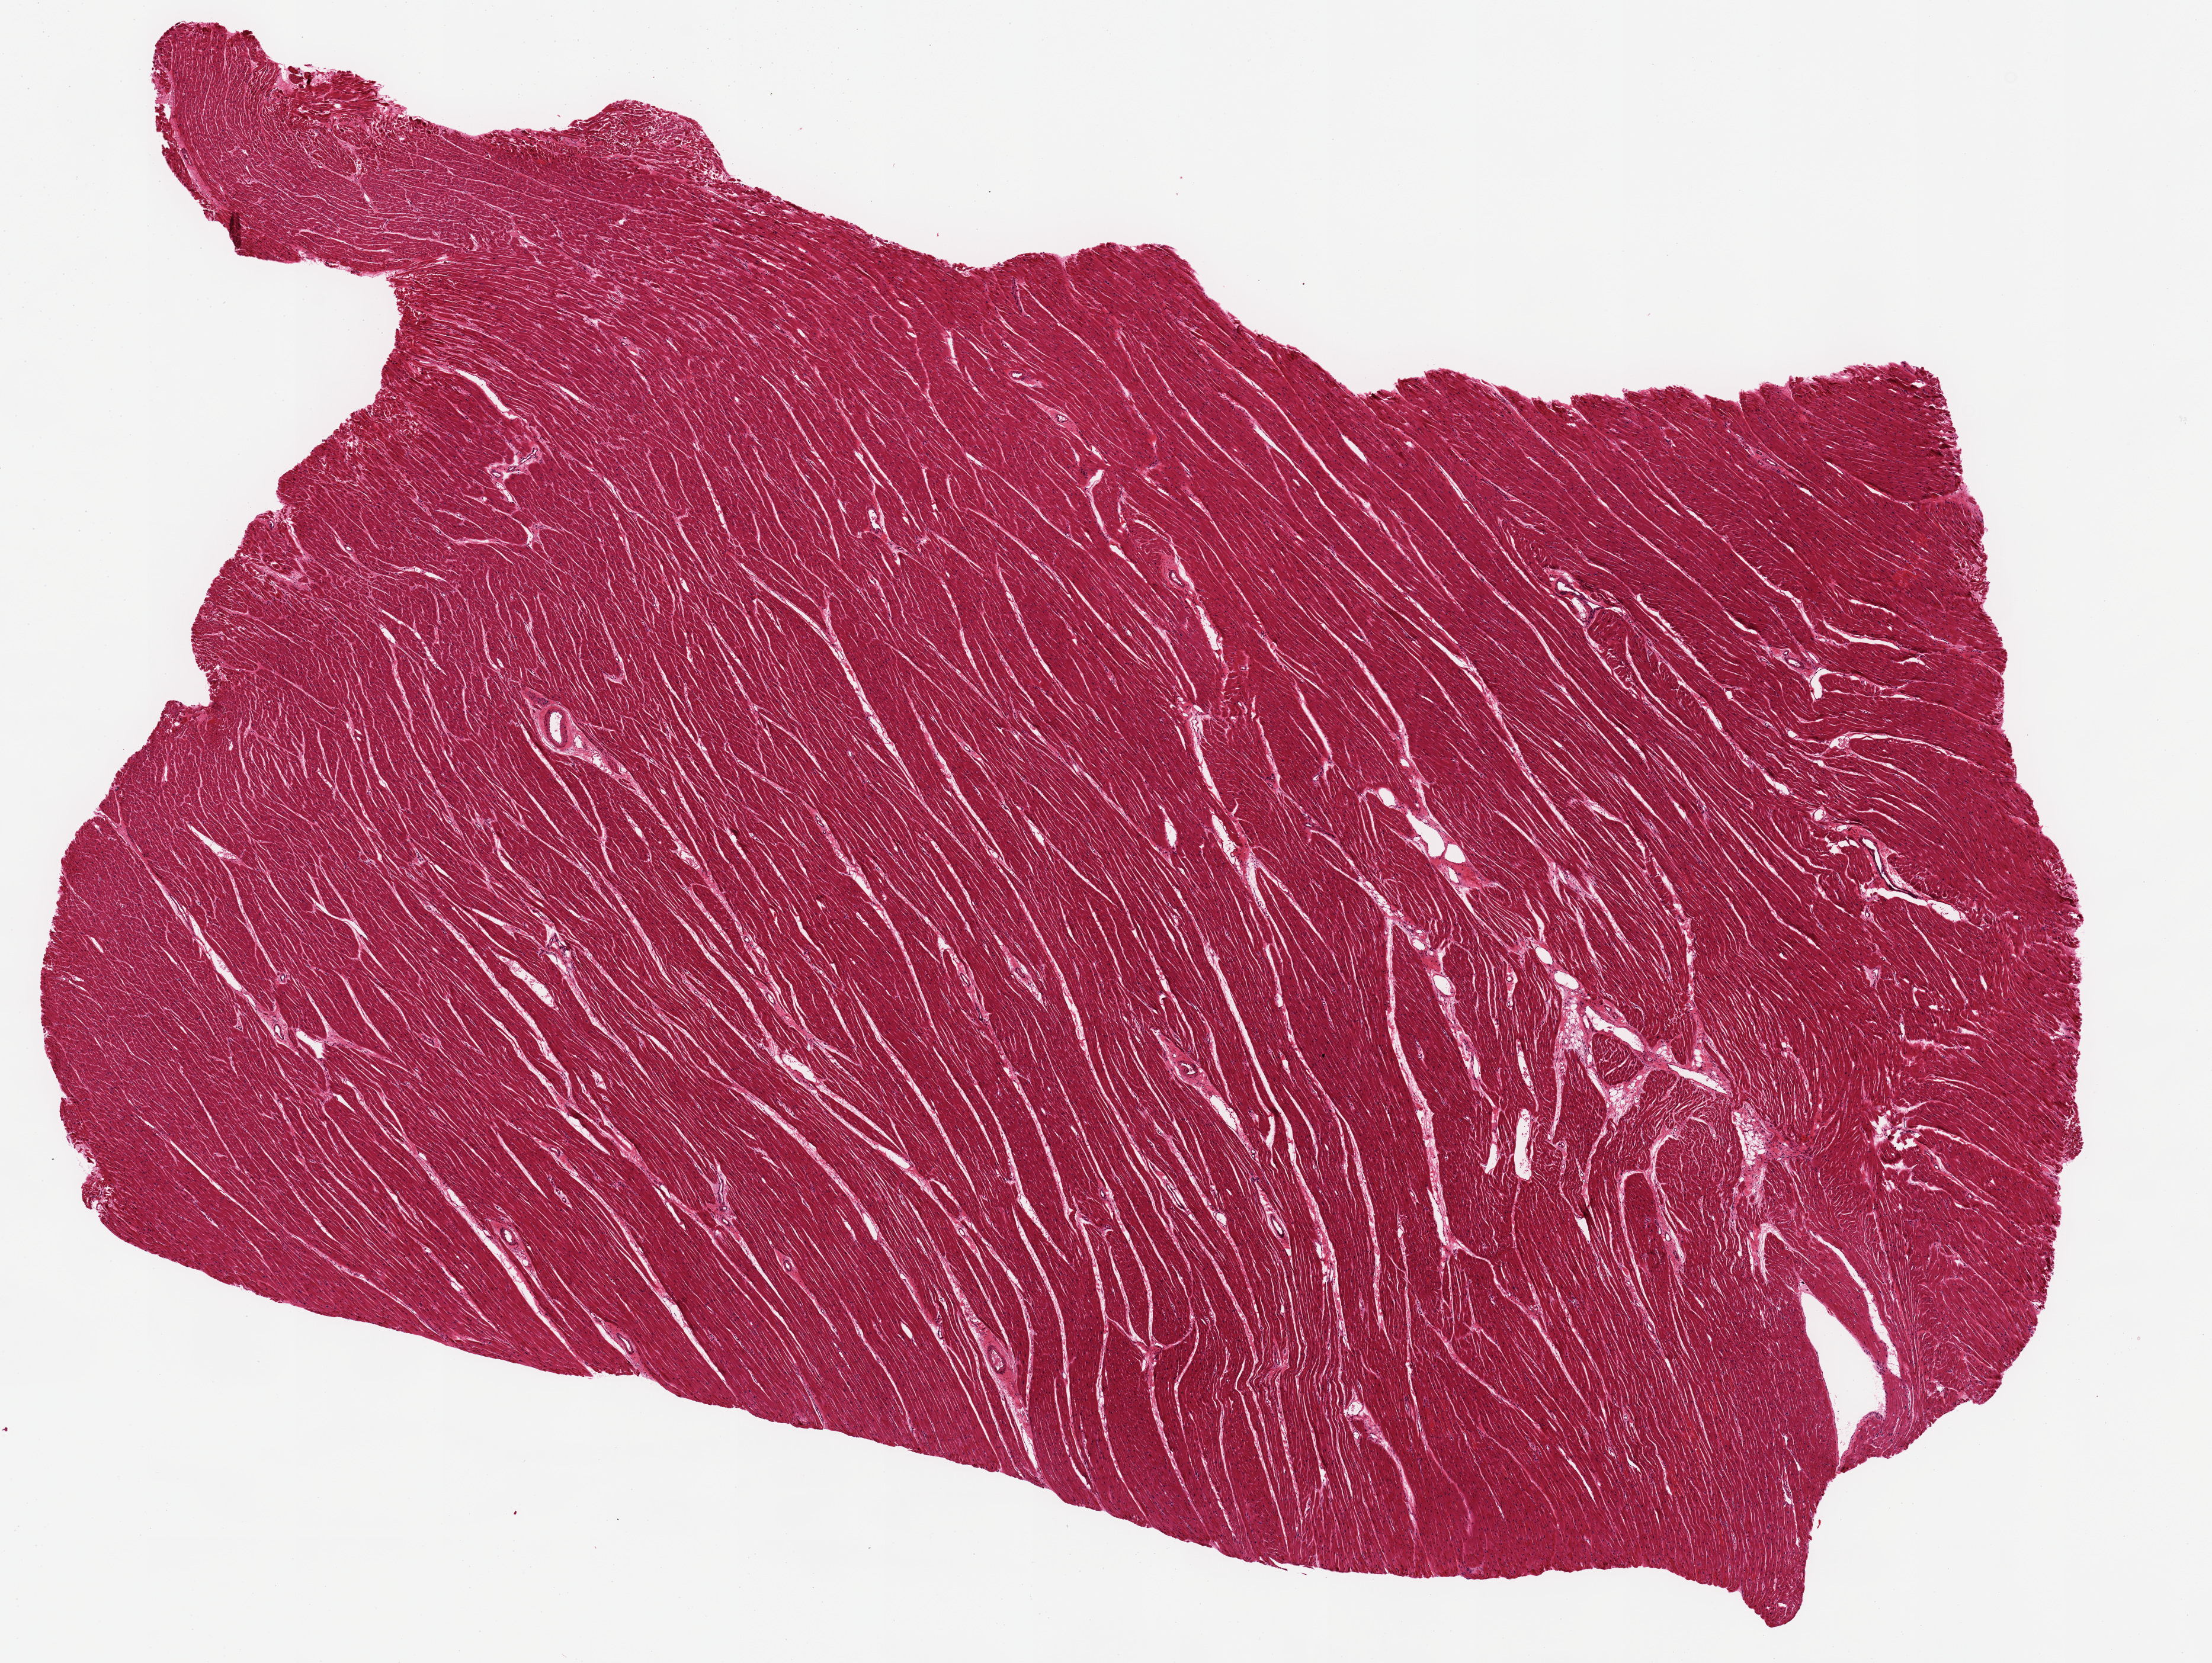
Digitized haematoxylin and eosin-stained section, shown as a low-resolution overview of the whole scanned area (about 14.8 x 11.1 mm, slide scanned at 20x). PAXgene-fixed paraffin-embedded (PFPE) section. Section of heart (target tissue). Donor tissue sample. Donor: male.
Pathologist's review note for this sample: 1 piece 13x8 mm.